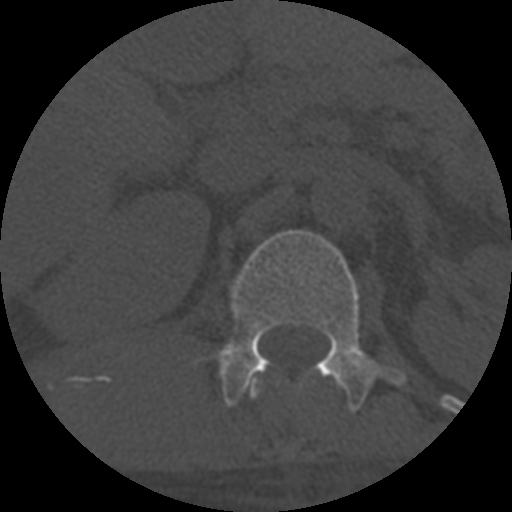
CT including the spine, one axial slice; slice 293 of 708 in the series (ordered by position); reconstruction kernel STANDARD; one of 3 acquisitions stored at this slice position; bone window (W 1800 / L 400 HU); 1.25 mm slice thickness; 512 × 512 image matrix, field of view 160 × 160 mm. Patient age 55 years. From the clinical record (not read from this slice): primary cancer: colon.
Structures marked on this image (semi-automatic segmentation, software-assisted and operator-edited):
- L1 vertebra: bounding box [x1, y1, x2, y2] px = [214, 230, 406, 412]
- T12 vertebra: [246, 377, 260, 399]